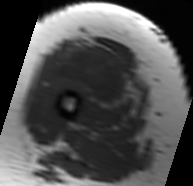
MRI of an extremity soft-tissue mass, one axial slice. Slice 26 of 91 in the series (ordered by position). MR volume resampled by the dataset authors to the PET/CT grid (not the native acquisition matrix). 193 × 186 image matrix, field of view 188 × 182 mm. Female patient. Case-level facts recorded for this patient, not image findings: histological type: malignant solitary fibrous tumor; grade: intermediate; site of the primary tumour: right thigh.
Outlined on this slice (expert contour drawn on MRI and transferred to this co-registered scan by the dataset authors):
- gross tumour volume including surrounding oedema: bounding box <47,37,144,113> (left, top, right, bottom; pixels)
- gross tumour volume (mass): <49,44,130,106>